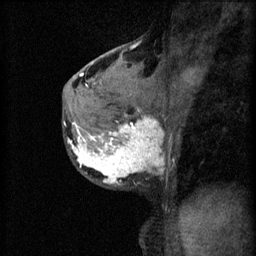
Breast MRI (dynamic contrast-enhanced), one sagittal slice; position 36 of 60 along the scan axis; 3 images stored at this slice position (order not interpretable as contrast timing); 1.5 T; TE 4.2 ms, TR 11 ms; 256 × 256 image matrix, field of view 180 × 180 mm. Female patient, age 37 years.
Structures marked on this image (semi-automatic segmentation, software-assisted and operator-edited):
- analysis volume of interest (the breast-tissue region the enhancement analysis was run in; not a lesion): bounding box [x1, y1, x2, y2] px = [68, 118, 168, 187]
- tumour enhancement mask (voxels above the 70 % enhancement threshold inside the analysis volume of interest): [68, 118, 163, 185]